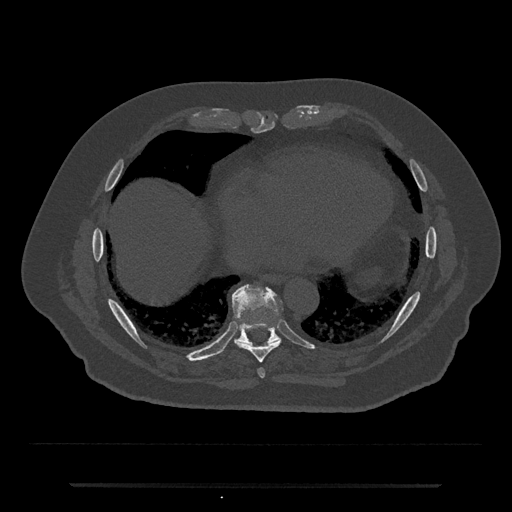
CT including the spine, one axial slice. Slice 788 of 797 in the series (ordered by position). Reconstruction kernel Br40s/3. Bone window (W 1800 / L 400 HU). 0.5 mm slice thickness. 512 × 512 image matrix, field of view 434 × 434 mm. Male patient, age 80 years. From the clinical record (not read from this slice): primary cancer: prostate; vertebrae with lytic lesions (as recorded): L1, T11.
Structures marked on this image (semi-automatically segmented with operator editing):
- T8 vertebra: bounding box [x1, y1, x2, y2] px = [236, 324, 280, 363]
- T9 vertebra: [223, 284, 283, 351]